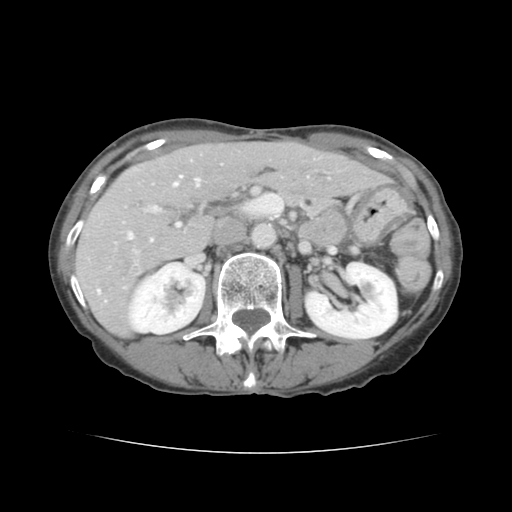
Contrast-enhanced abdominal CT, one axial slice; position 70 of 136 along the scan axis; 120 kVp; intravenous contrast given; soft-tissue window (W 400 / L 40 HU); 2.5 mm slice thickness; 512 × 512 image matrix, field of view 319 × 319 mm. Female patient, age 77 years. From the clinical record (not read from this slice): diagnosis: colorectal cancer liver metastases, imaged before liver resection; multiple liver metastases: yes; largest metastasis: 3 cm; disease in both lobes: no.
Outlined on this slice (outlined manually by an expert reader):
- hepatic veins: bounding box [x1, y1, x2, y2] px = [128, 175, 200, 239]
- liver: [76, 143, 385, 335]
- planned liver remnant (the part of the liver to remain after resection): [158, 143, 385, 201]
- portal vein (with intrahepatic branches): [98, 206, 180, 293]